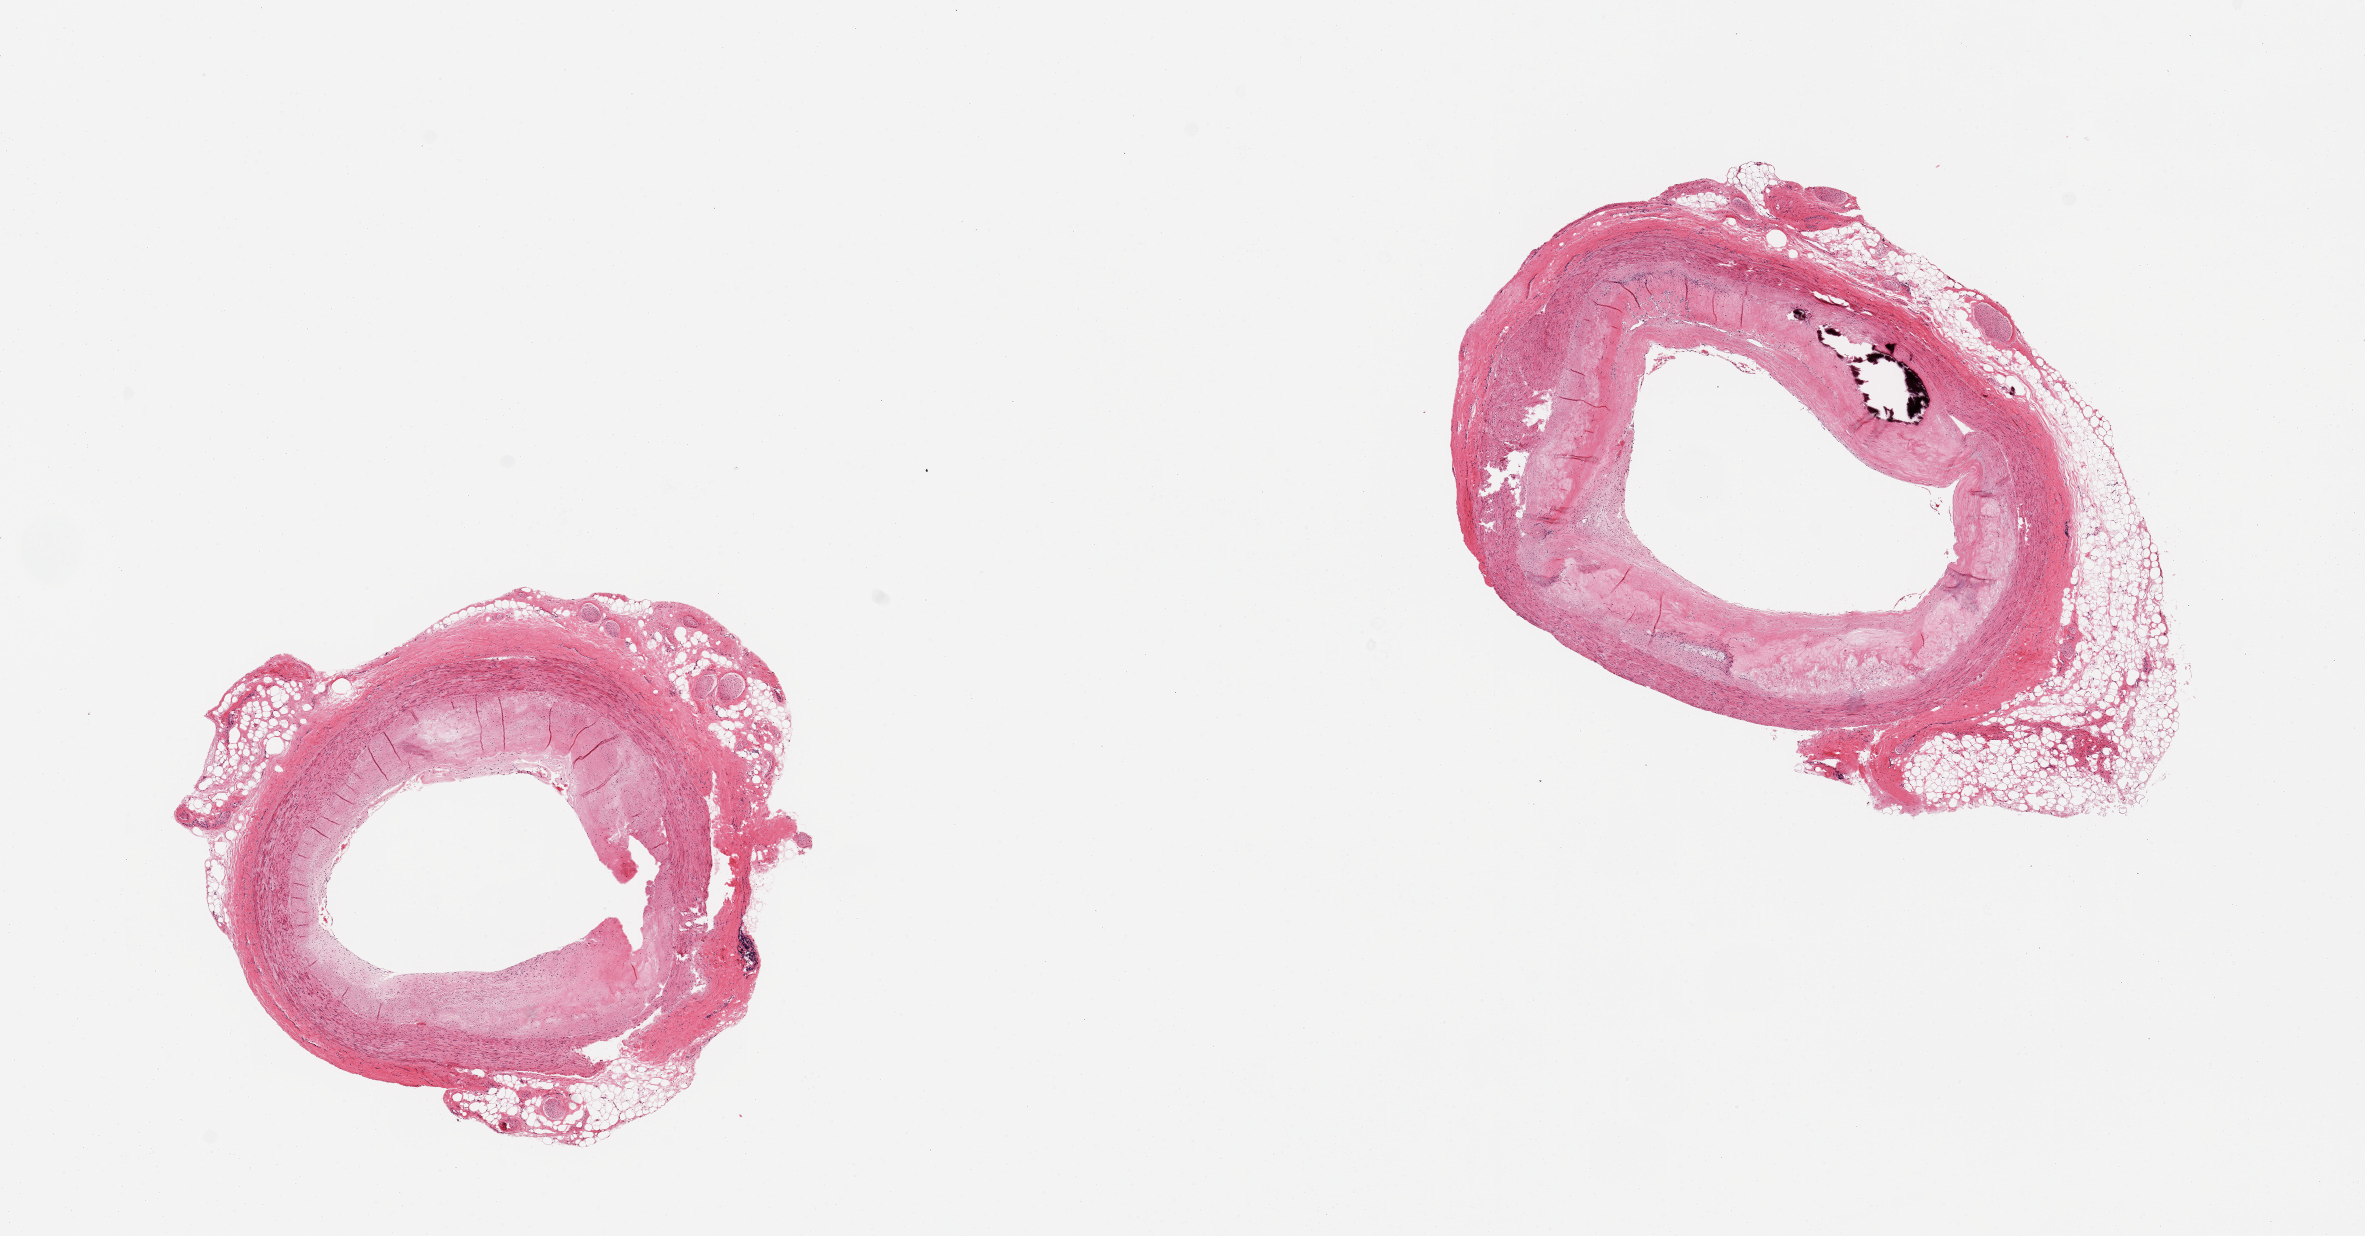
Hematoxylin and eosin (H&E) whole-slide image — a low-resolution overview of the entire scanned area, about 18.7 x 9.8 mm, PAXgene-fixed, paraffin-embedded tissue, section of coronary artery (target tissue), tissue donor sample. Donor sex: male.
- review note (as recorded): 2 pieces; calcific atherosclerosis with concentric narrowing of the lumen, attached fat/nerve (30%)